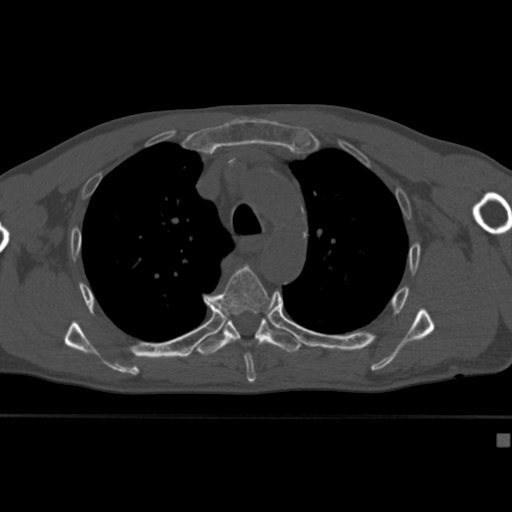
CT including the spine, one axial slice; position 303 of 430 along the scan axis; reconstruction kernel Br40s; 120 kVp; bone window (W 1800 / L 400 HU); 512 × 512 image matrix, field of view 337 × 337 mm. Patient: male, 64 years. From the clinical record (not read from this slice): primary cancer: uterus.
Outlined on this slice (semi-automatic segmentation, software-assisted and operator-edited):
- T5 vertebra: bounding box <206,265,276,382> (left, top, right, bottom; pixels)
- T6 vertebra: <196,314,302,357>